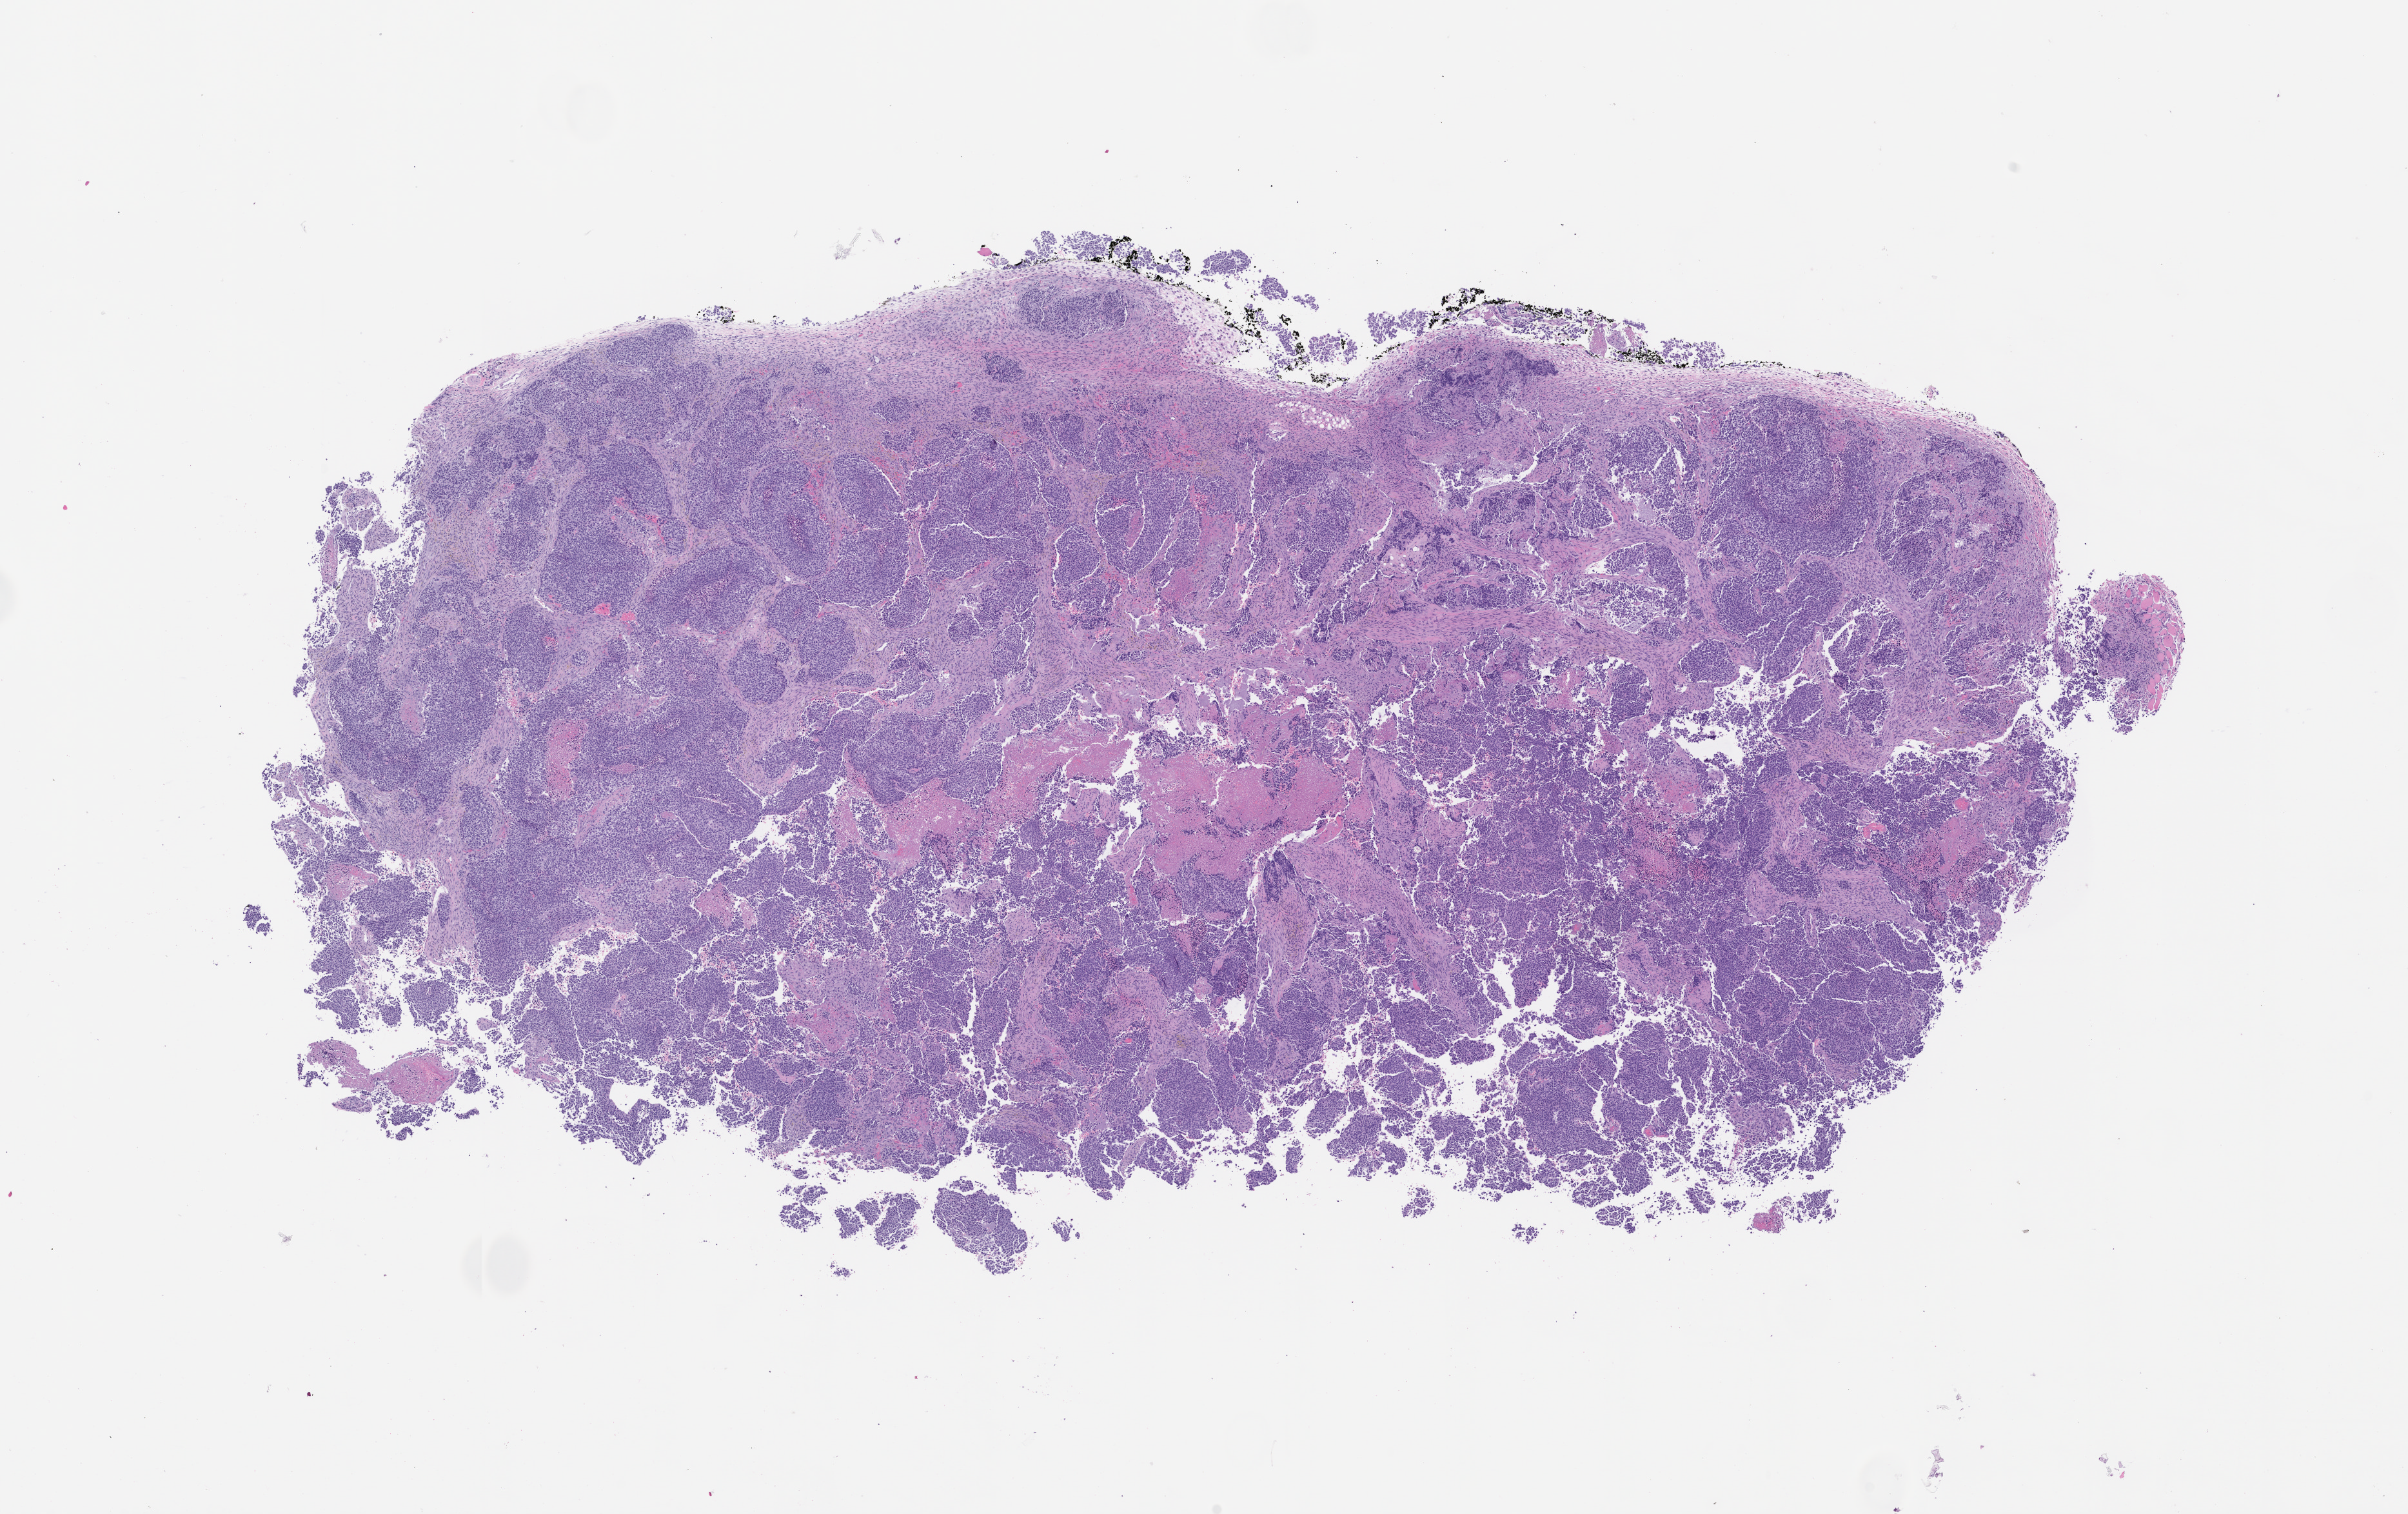
Haematoxylin and eosin whole-slide image of a patient-derived xenograft (PDX) tumor grown in a mouse — low-resolution overview of the scanned area, about 15.0 x 9.4 mm; formalin-fixed paraffin-embedded section; originating tumor site category: lung.
* originating patient diagnosis: Lung Adenocarcinoma